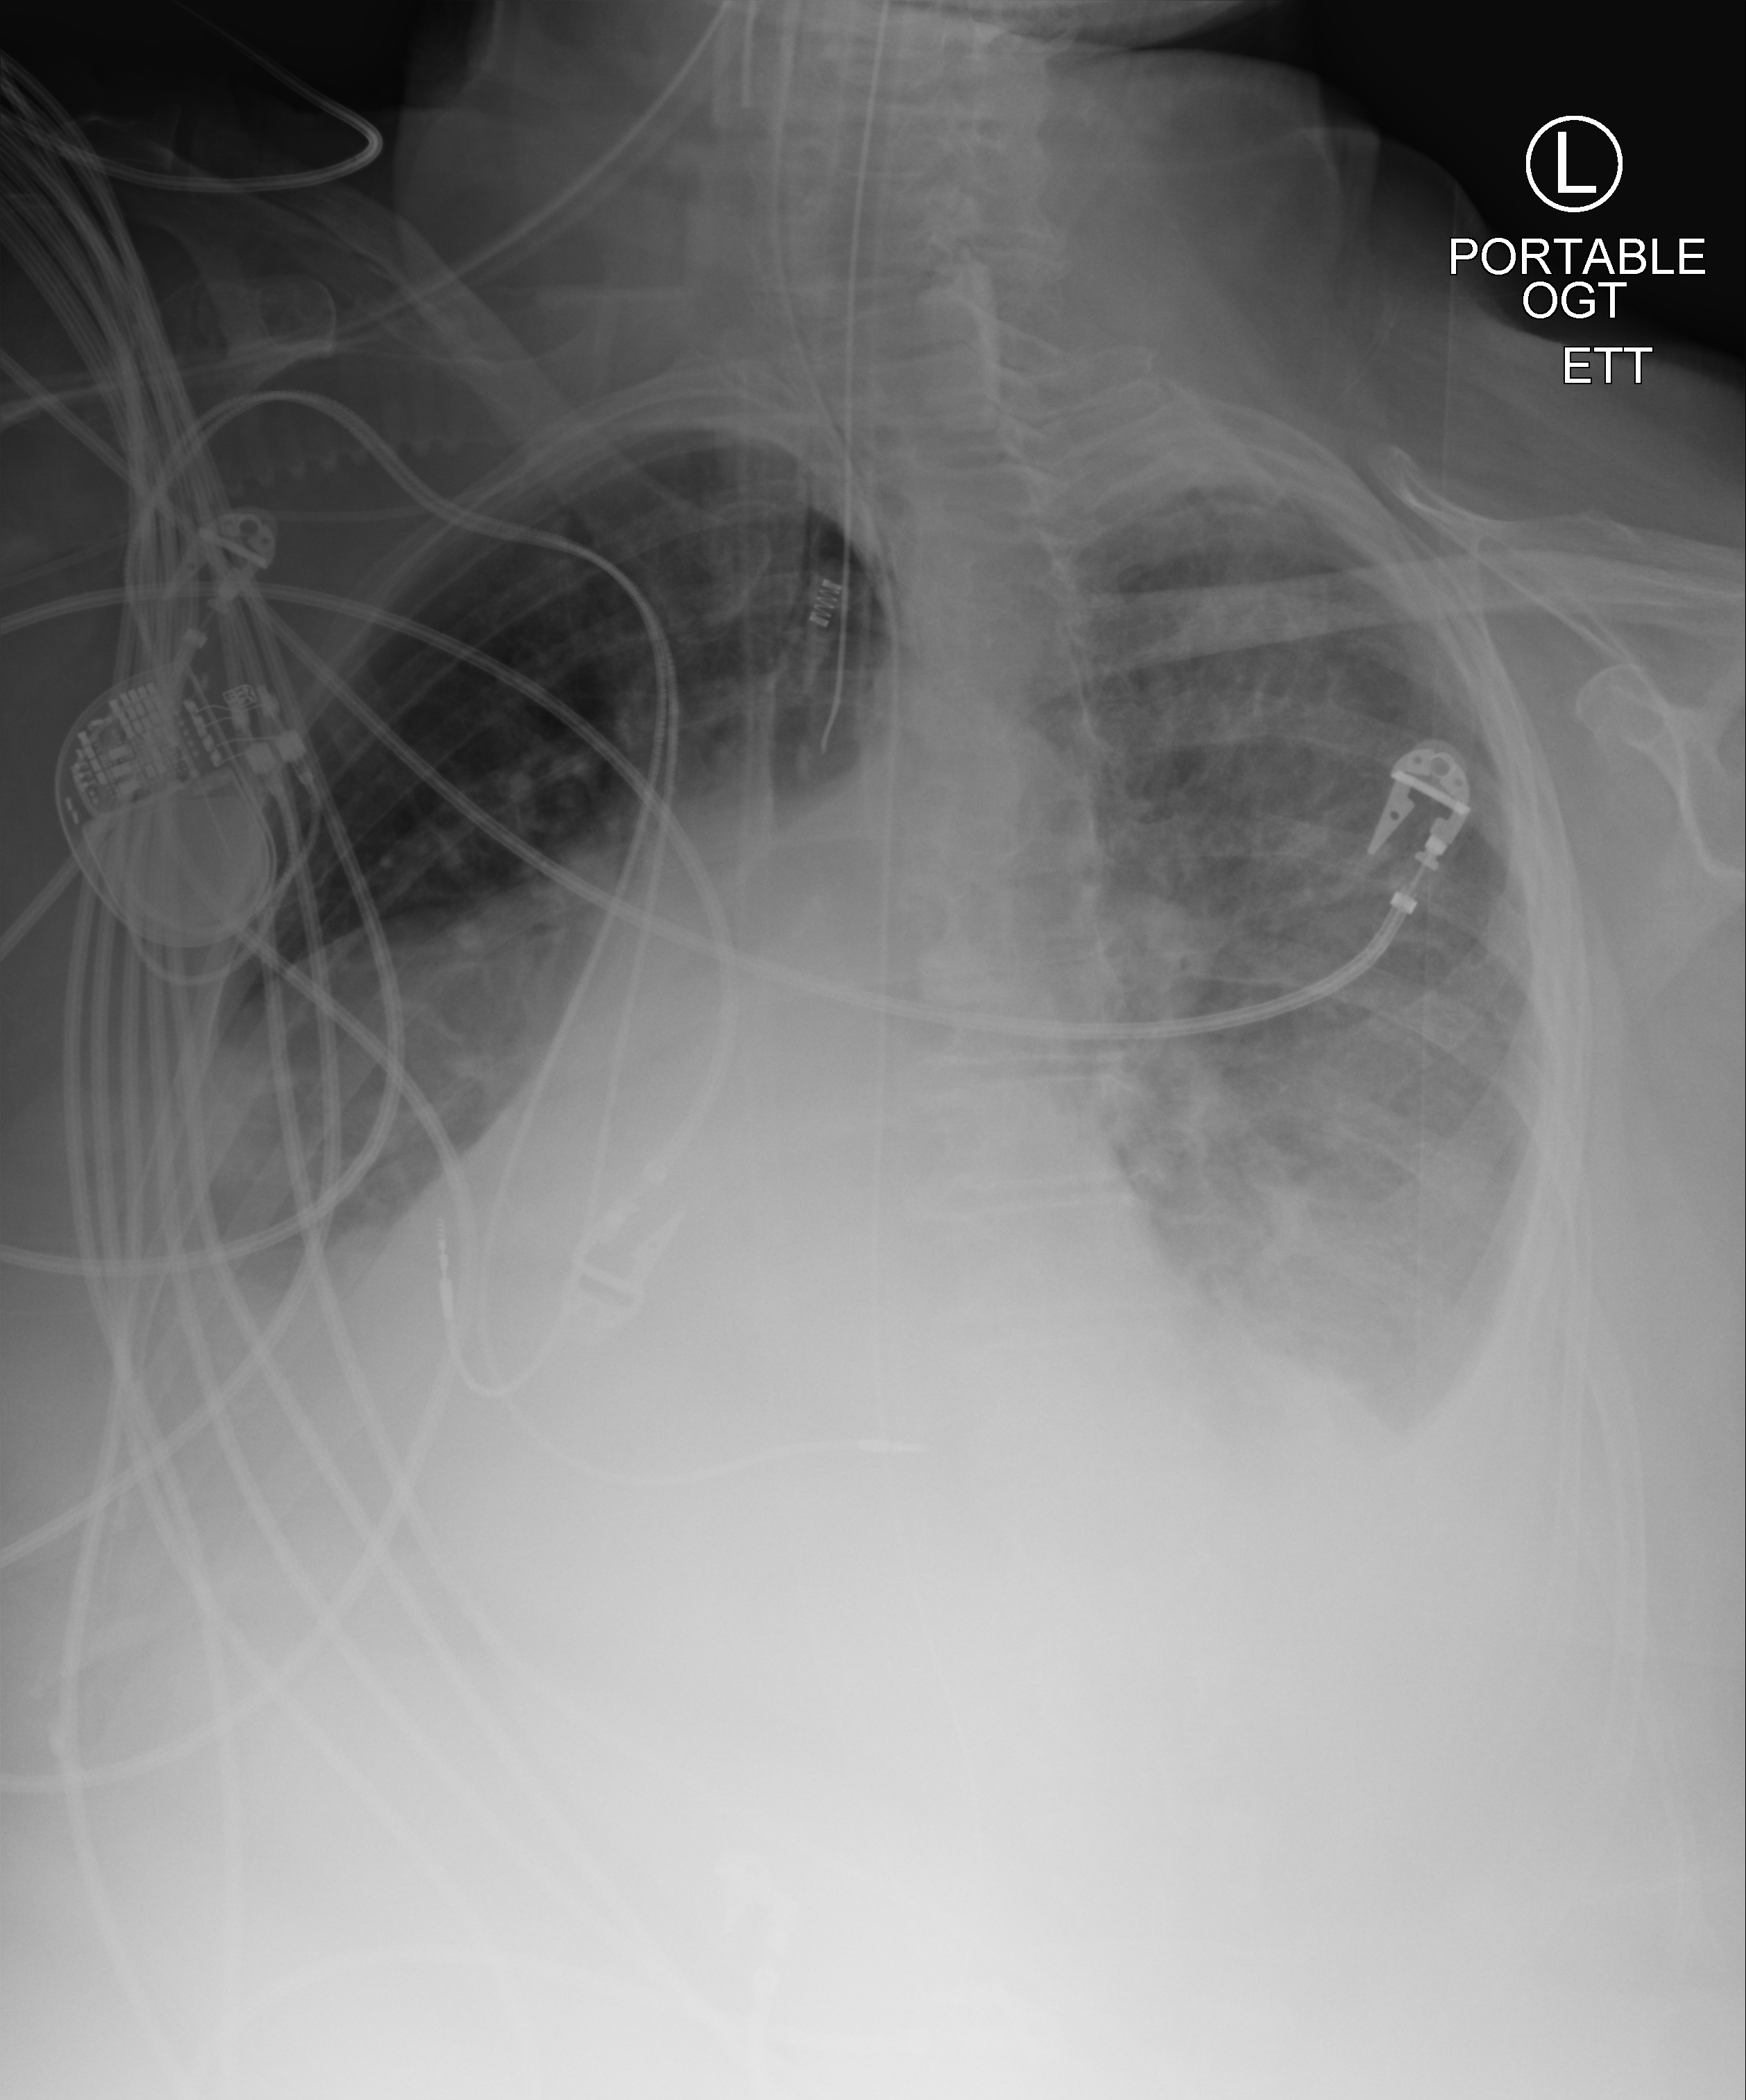
Chest X-ray (portable), anteroposterior (AP) projection. Patient hospitalised with COVID-19; female, aged 75–90 years.
Hospital-stay facts (about this admission, not read from this image; timing relative to this image not recorded): COPD (admission record): yes; mechanically ventilated during this hospital stay: yes; admitted to intensive care during this hospital stay: yes.